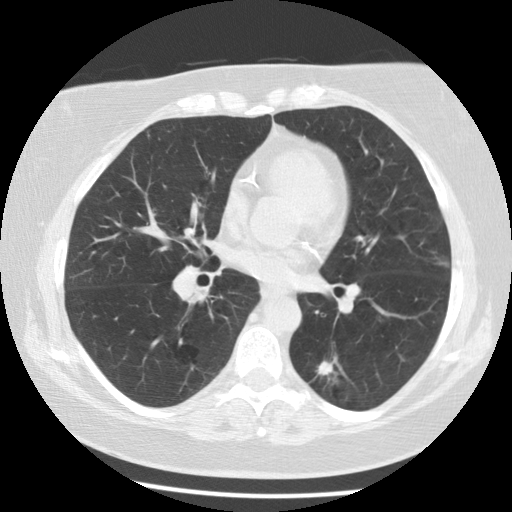
Low-dose screening chest CT, axial slice, third annual screen, lung window (W 1500 / L -600 HU), slice 60 of 116 in the series, 512 × 512 image matrix, field of view 341 × 341 mm. Female participant, aged 59 years at enrolment. Current smoker at enrolment.
Expert reader's lesion annotation, box from (x=291, y=348) to (x=357, y=406) px. The screening reader recorded 6 non-calcified nodules or masses ≥4 mm on this exam; which of them this box marks is not recorded. Official screen result: positive, other. Lung cancer was diagnosed 56 days after this screen: adenocarcinoma, NOS, left lower lobe, poorly differentiated (G3), stage IA (AJCC 6th edition), 15 mm at pathology.